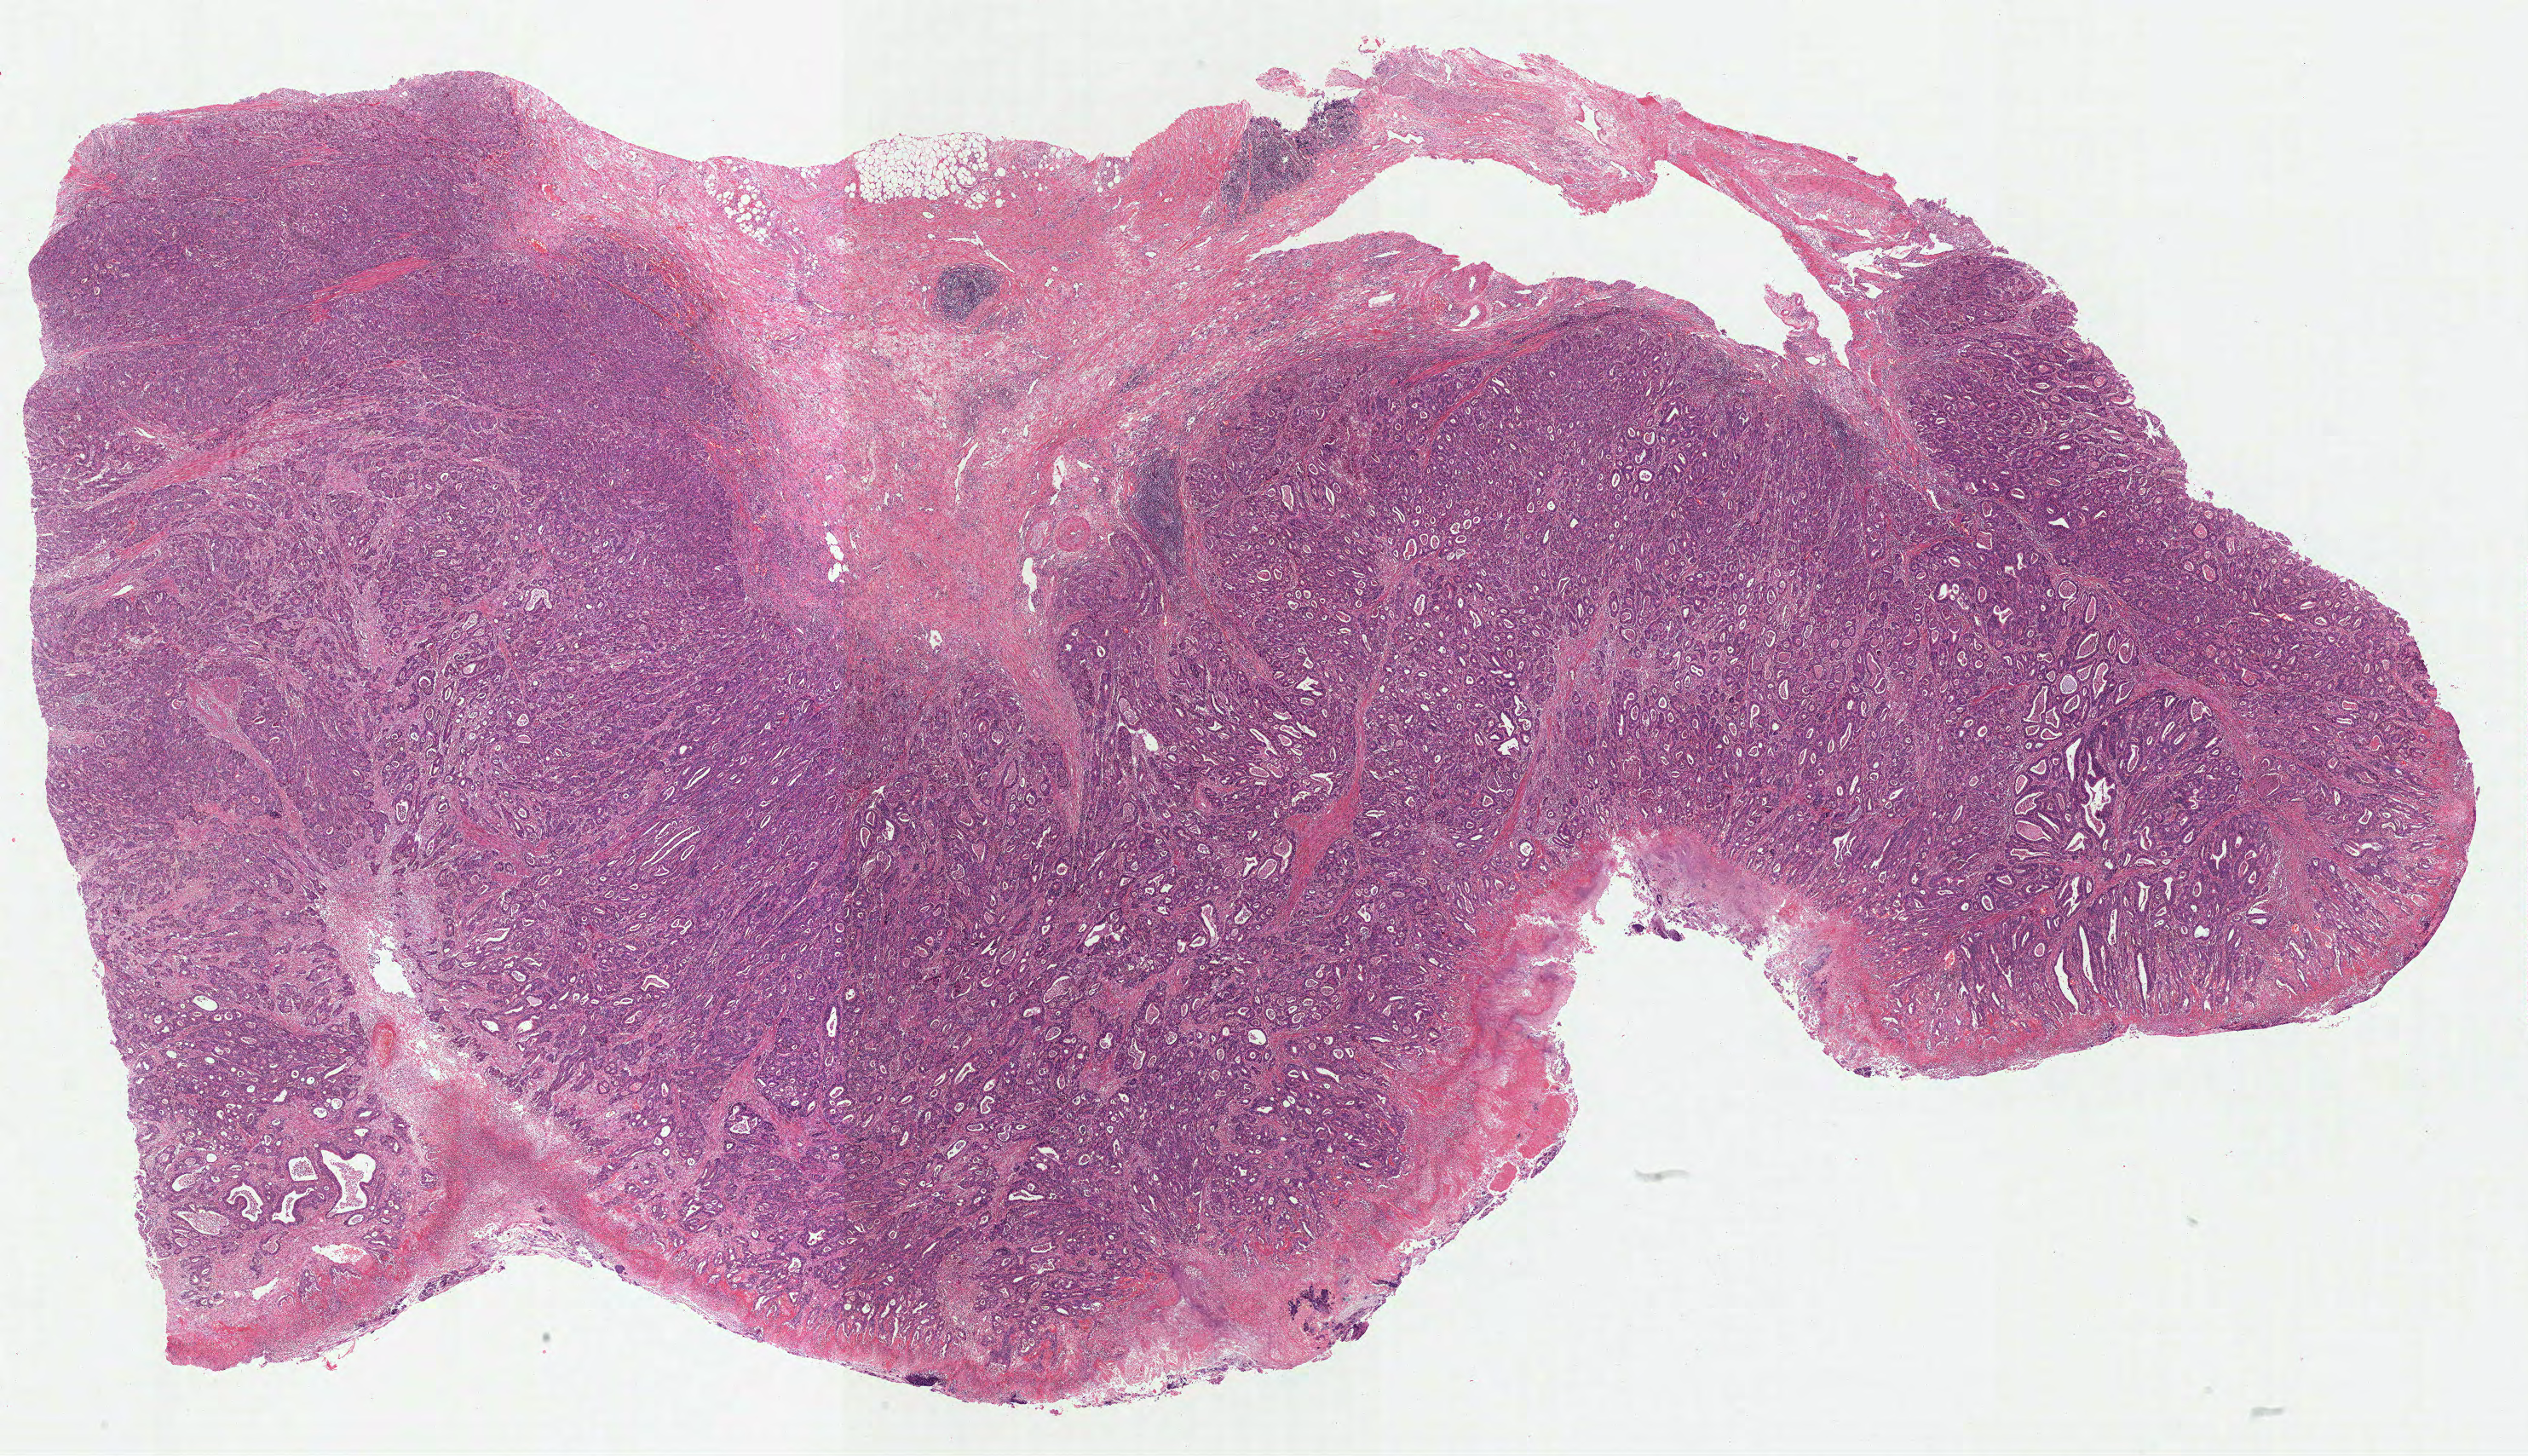
Digitized H&E-stained tissue section (whole slide) — whole scanned area (about 23.9 x 13.8 mm, slide scanned at 40x) shown as a low-resolution overview, FFPE section, primary tumour sample from the stomach. Male, age 66 years at initial diagnosis. Histologic grade: G2 (moderately differentiated).
Pathologic diagnosis: Adenocarcinoma, intestinal type (fundus of stomach). Lymph nodes positive (case pathology): 0 of 15 examined. AJCC pathologic stage: IIA.